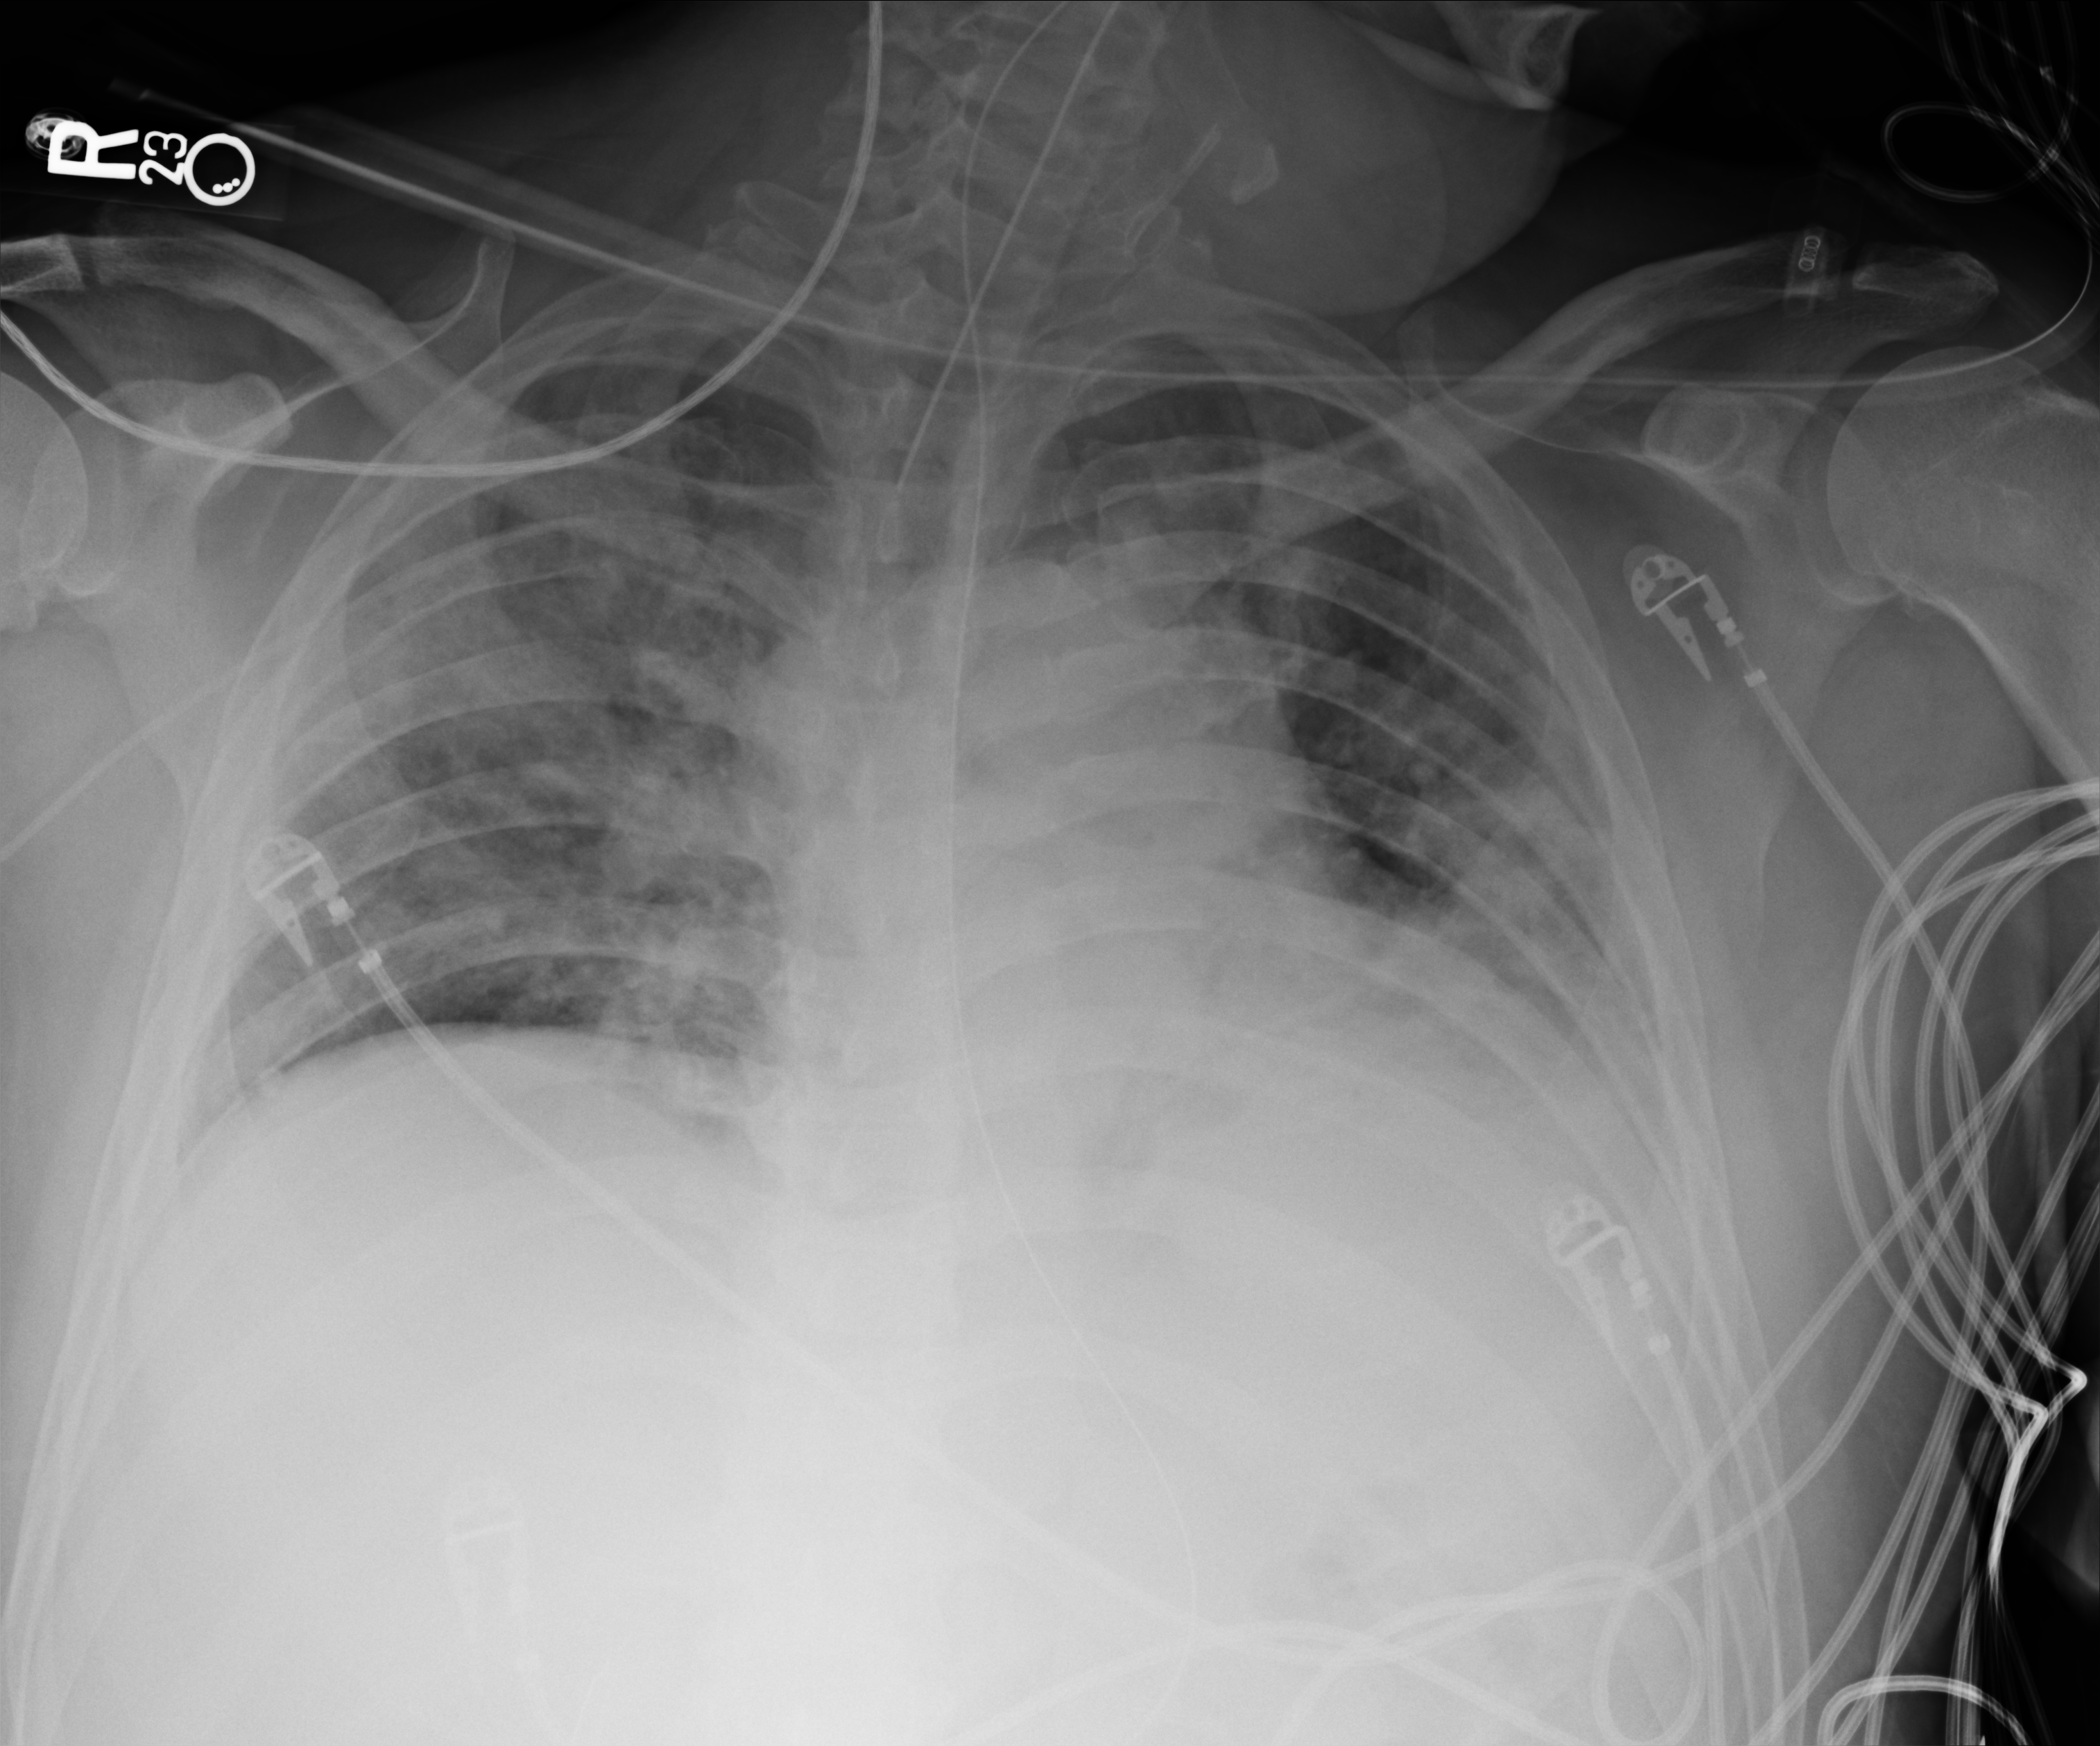
Portable chest radiograph, anteroposterior (AP) projection. Male patient hospitalised with COVID-19, age 18–59 years.
From the hospital-stay record, not from the radiograph (when in the stay this image was taken is not recorded): other chronic lung disease (admission record): no.